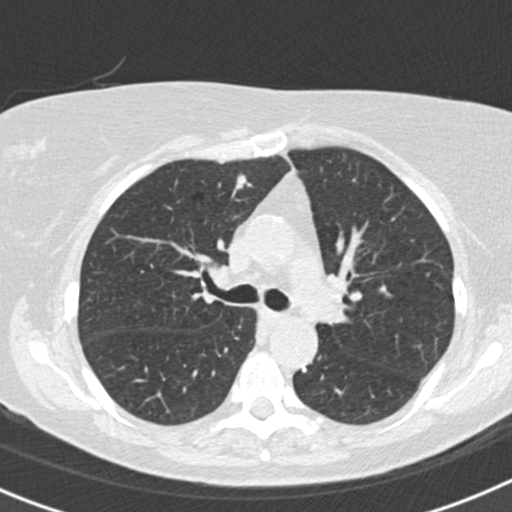
Chest CT (low-dose screening protocol), one axial image; second screening round (one year after baseline); lung window (W 1500 / L -600 HU); standard (soft-tissue) reconstruction kernel (B30f); 120 kVp. Female, age 72 years at enrolment. Former smoker at enrolment.
• Expert-annotated lung lesion, bounding box (x1, y1, x2, y2) in pixels: (215, 163, 261, 208).
• The exam's reader record, not a measurement of the box and not confirmed to be the same lesion: non-calcified nodule or mass ≥4 mm, right upper lobe, 5 × 5 mm, smooth margins, soft tissue attenuation.
• Official screen result: positive, other.
• Participant outcome: lung cancer diagnosed 462 days after this screen — adenocarcinoma, NOS, right upper lobe, moderately differentiated (G2), stage IA (AJCC 6th edition), 15 mm at pathology.